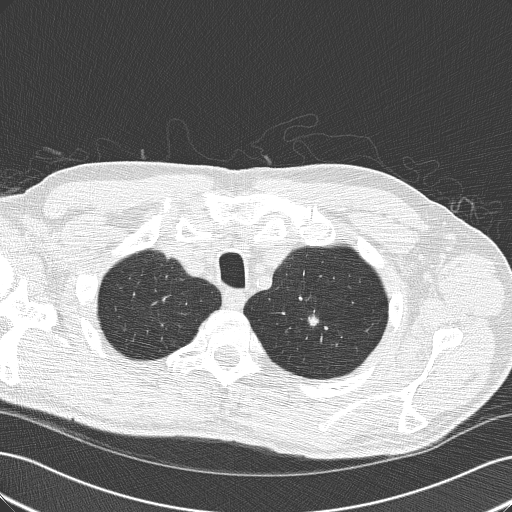
Axial slice from a low-dose chest CT screening exam. Third screening round (two years after baseline). Lung window (W 1500 / L -600 HU). 2 mm slice thickness. Lung (sharp) reconstruction kernel (B50f). Slice 33 of 192 in the series. Male participant, aged 64 years at enrolment. Former smoker at enrolment.
Expert reader's lesion annotation, bounding box <290,302,332,343> (left, top, right, bottom; pixels). Screening reader's record for this exam (one nodule recorded; not confirmed to be the boxed lesion): non-calcified nodule or mass ≥4 mm, left upper lobe, 8 × 8 mm, smooth margins, soft tissue attenuation, pre-existing on the prior screen: yes; interval growth: yes. Later outcome: lung cancer diagnosed 111 days after this screen — adenocarcinoma, NOS, left upper lobe, poorly differentiated (G3), stage IA (AJCC 6th edition), 10 mm at pathology.